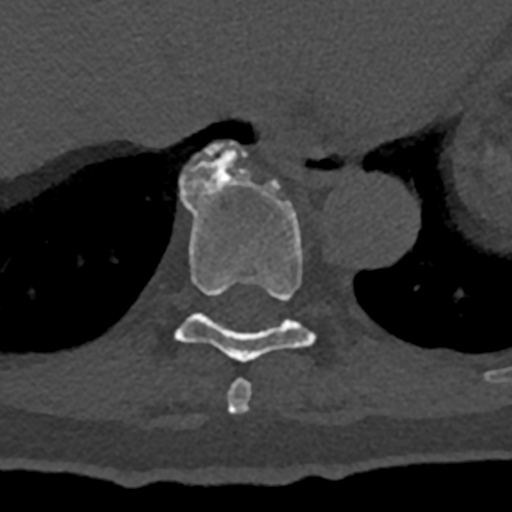
CT including the spine, one axial slice. Position 653 of 797 along the scan axis. Reconstruction kernel Br40s/3. Bone window (W 1800 / L 400 HU). 512 × 512 image matrix, field of view 160 × 160 mm. Patient: male, 74 years. From the clinical record (not read from this slice): primary cancer: renal; vertebrae with lytic lesions (as recorded): T10, L1, L2, L3, L4, L5.
Structures marked on this image (semi-automatically segmented with operator editing):
- T10 vertebra: bounding box (x1, y1, x2, y2) in pixels: (179, 142, 247, 195)
- T8 vertebra: (227, 379, 252, 414)
- T9 vertebra: (174, 153, 315, 362)